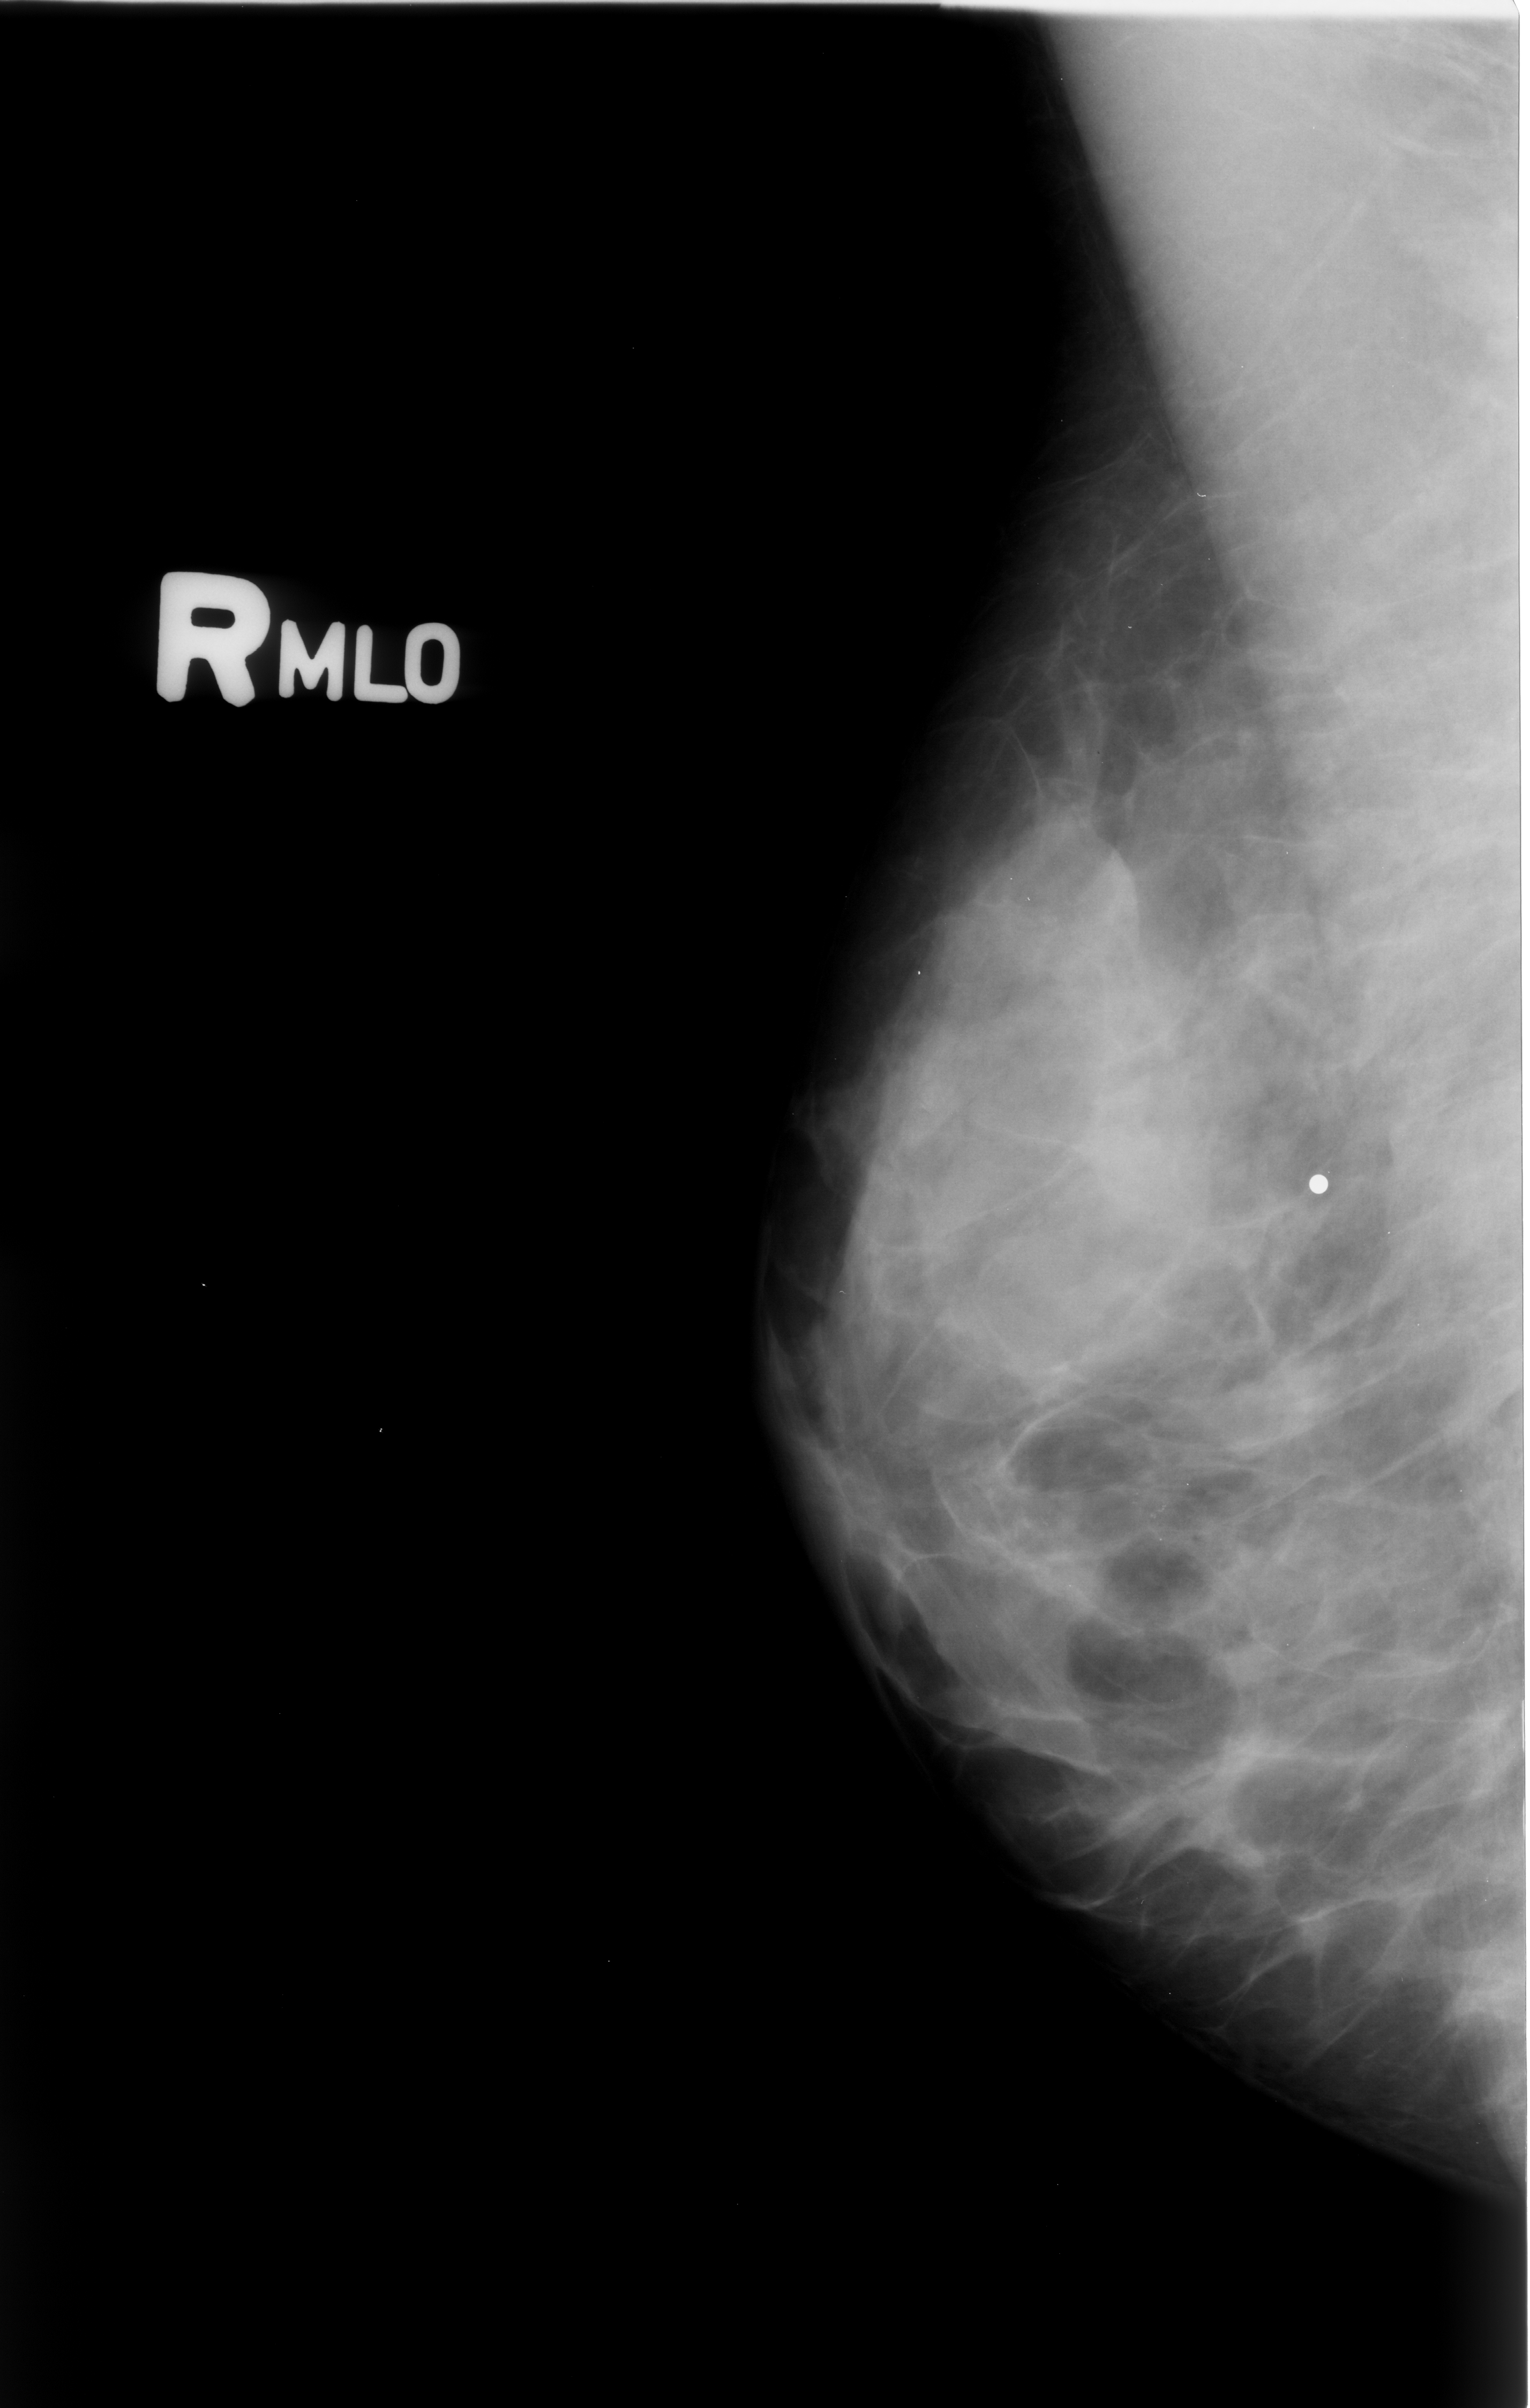
Digitized screen-film mammogram, right breast, mediolateral oblique (MLO) view, breast composition: heterogeneously dense (BI-RADS density category 3 of 4).
Calcifications, morphology pleomorphic, distribution clustered; BI-RADS assessment category 4; subtlety rating 3 on a 1 (subtle) to 5 (obvious) scale; pathology result (as recorded, not read from the image): benign.